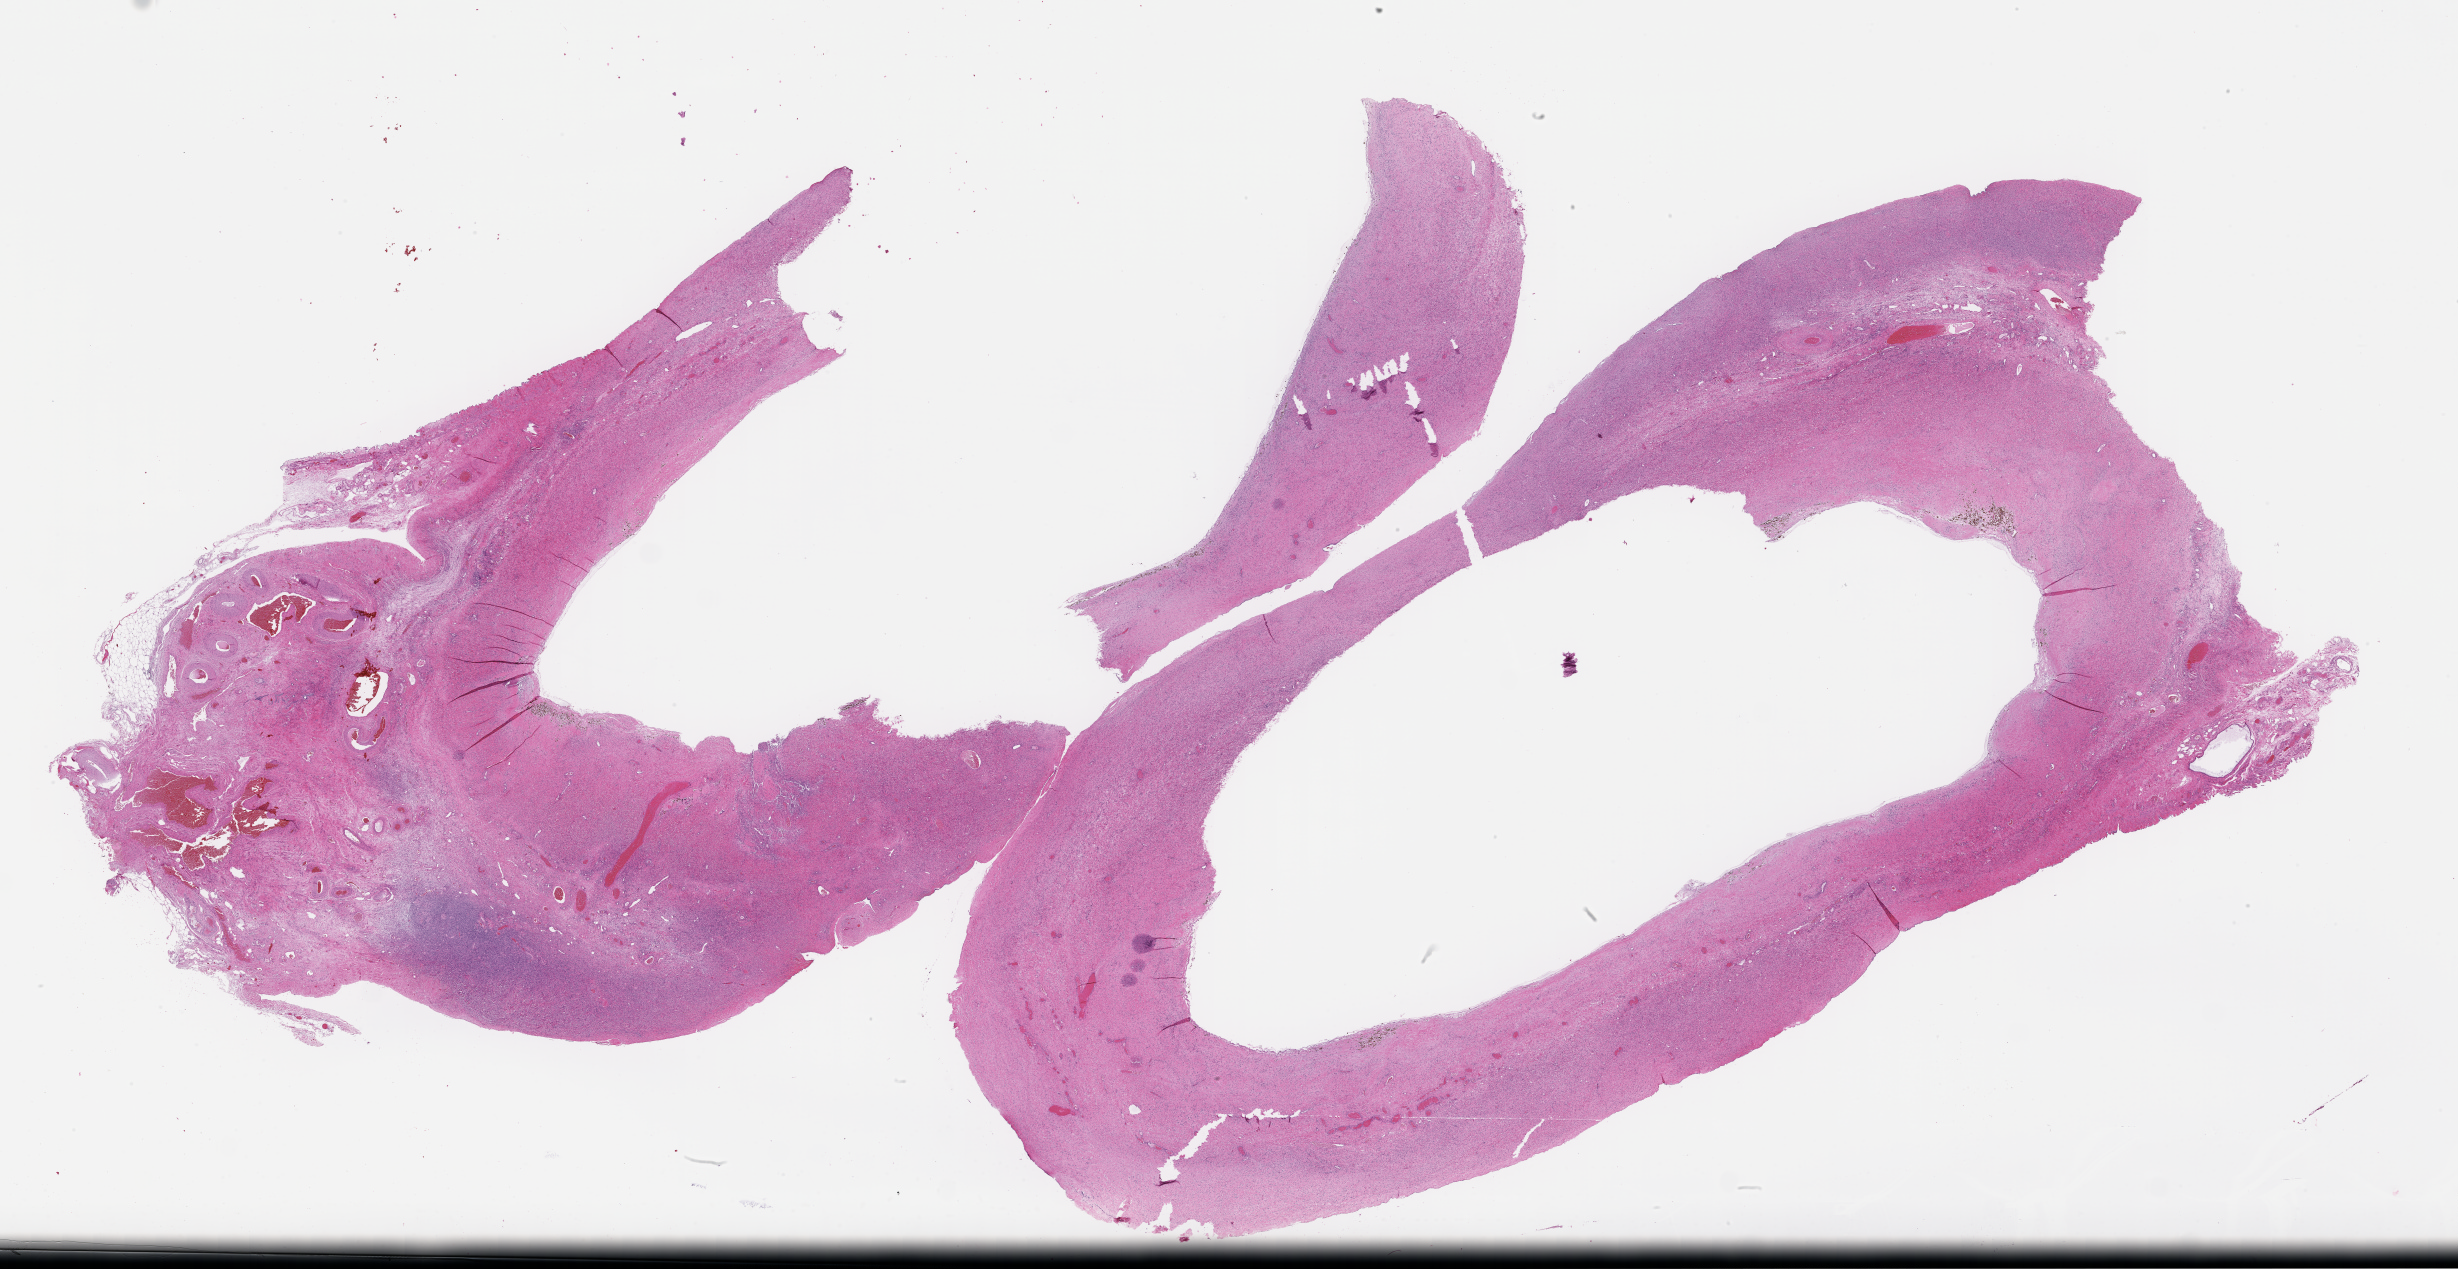
Whole-slide image, haematoxylin and eosin stain, low-resolution overview of the scanned area, about 39.7 x 20.5 mm; FFPE section; site: ovary; archival tissue. Patient: female.
This section: primary tumor. Diagnosis: Ovarian Carcinoma.